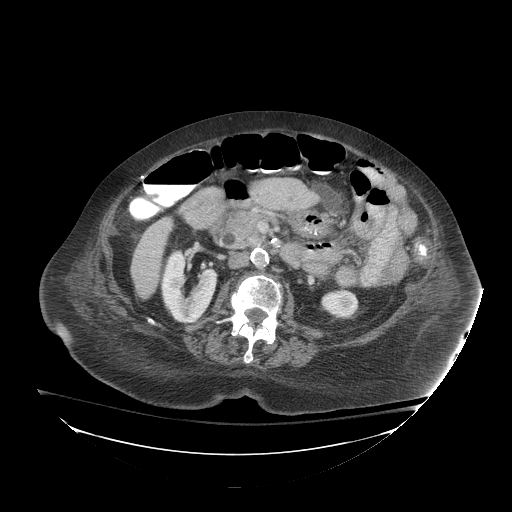
Contrast-enhanced abdominal CT (liver protocol), one axial slice; position 25 of 81 along the scan axis; soft-tissue window (W 400 / L 40 HU); 2.5 mm slice thickness; 512 × 512 image matrix, field of view 500 × 500 mm. Case-level facts recorded for this patient, not image findings: diagnosis: hepatocellular carcinoma (patient treated with transarterial chemoembolisation; whether this scan precedes or follows treatment is not stated here); TNM stage (as recorded): Stage-I; Child-Pugh class: B; tumour differentiation: well-moderately differentiated.
Structures marked on this image (semi-automatic segmentation, software-assisted and operator-edited):
- liver parenchyma outside the tumour (the mass and vessels are separate outlines, so this box may not span the whole liver): bounding box <132,218,172,272> (left, top, right, bottom; pixels)